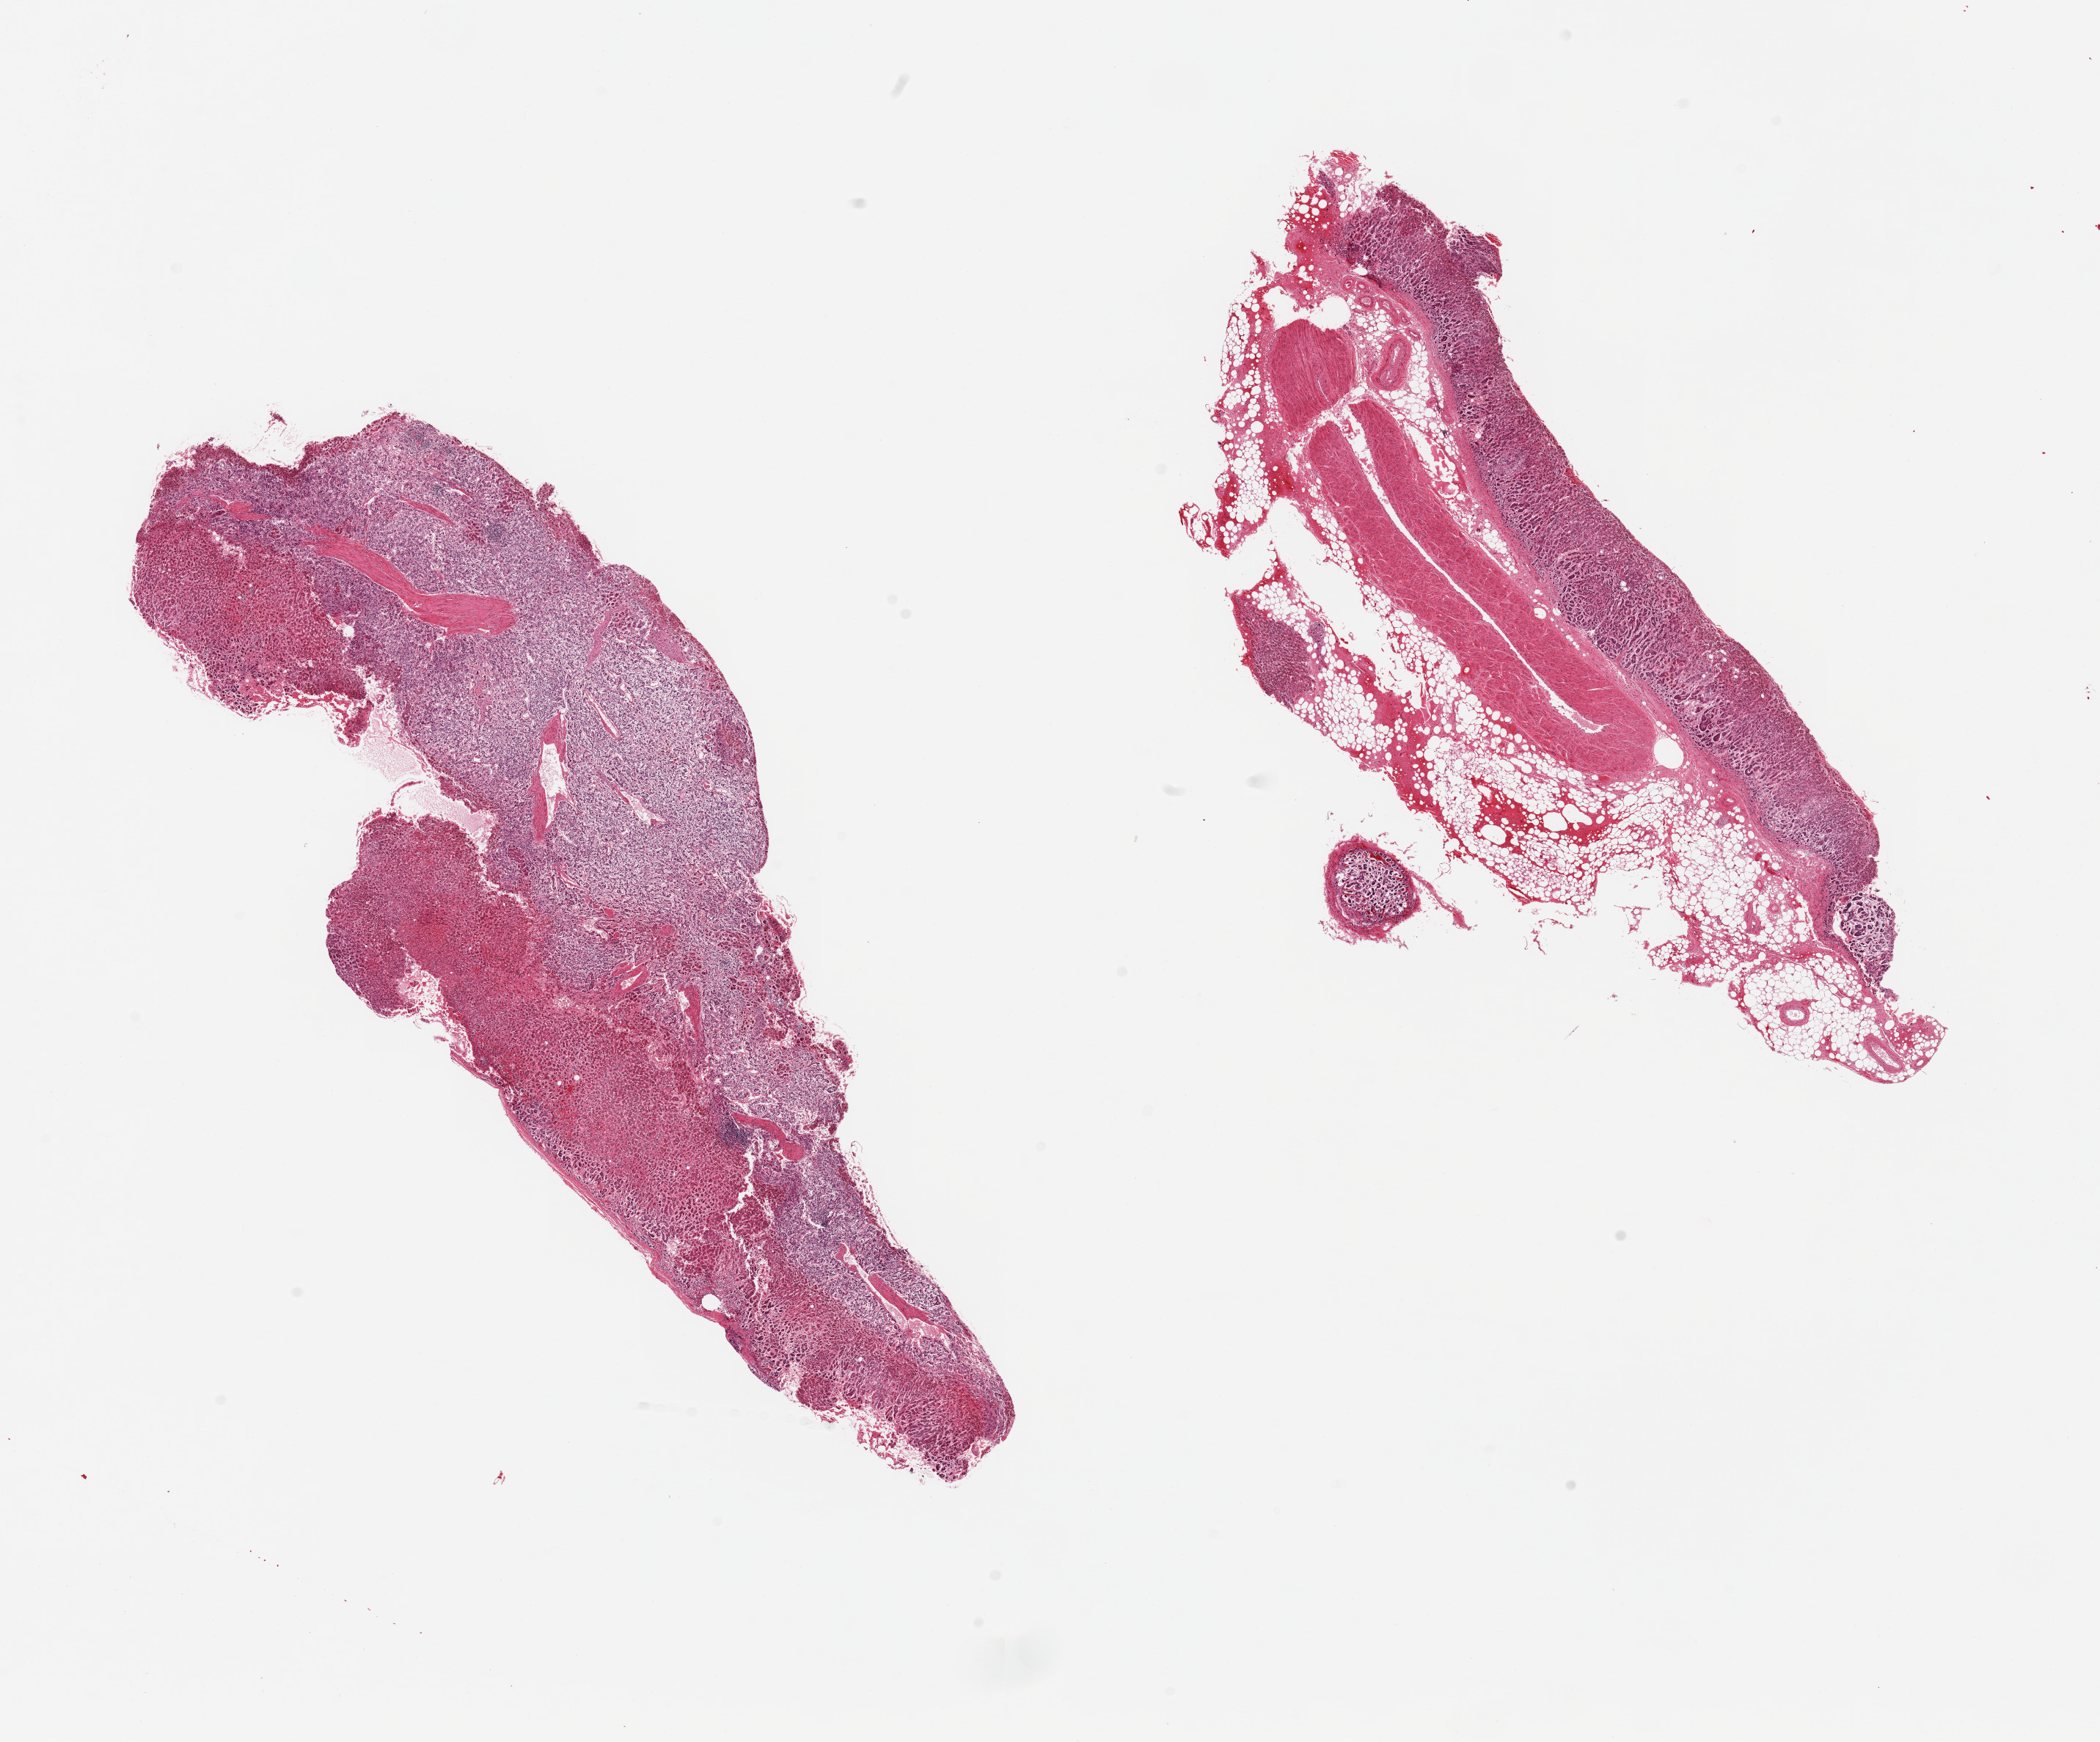
Whole-slide image, haematoxylin and eosin stain — a low-resolution overview of the entire scanned area, about 22.6 x 18.8 mm (slide scanned at 20x). PAXgene-fixed paraffin-embedded (PFPE) section. Sampled site (target tissue): adrenal gland. Donor tissue sample. Male donor.
Pathologist's review note for this sample: 2 pieces, one section is ~60% adherent fat/vessel; Other may have medualla, but poorly preserved/autolyzed.